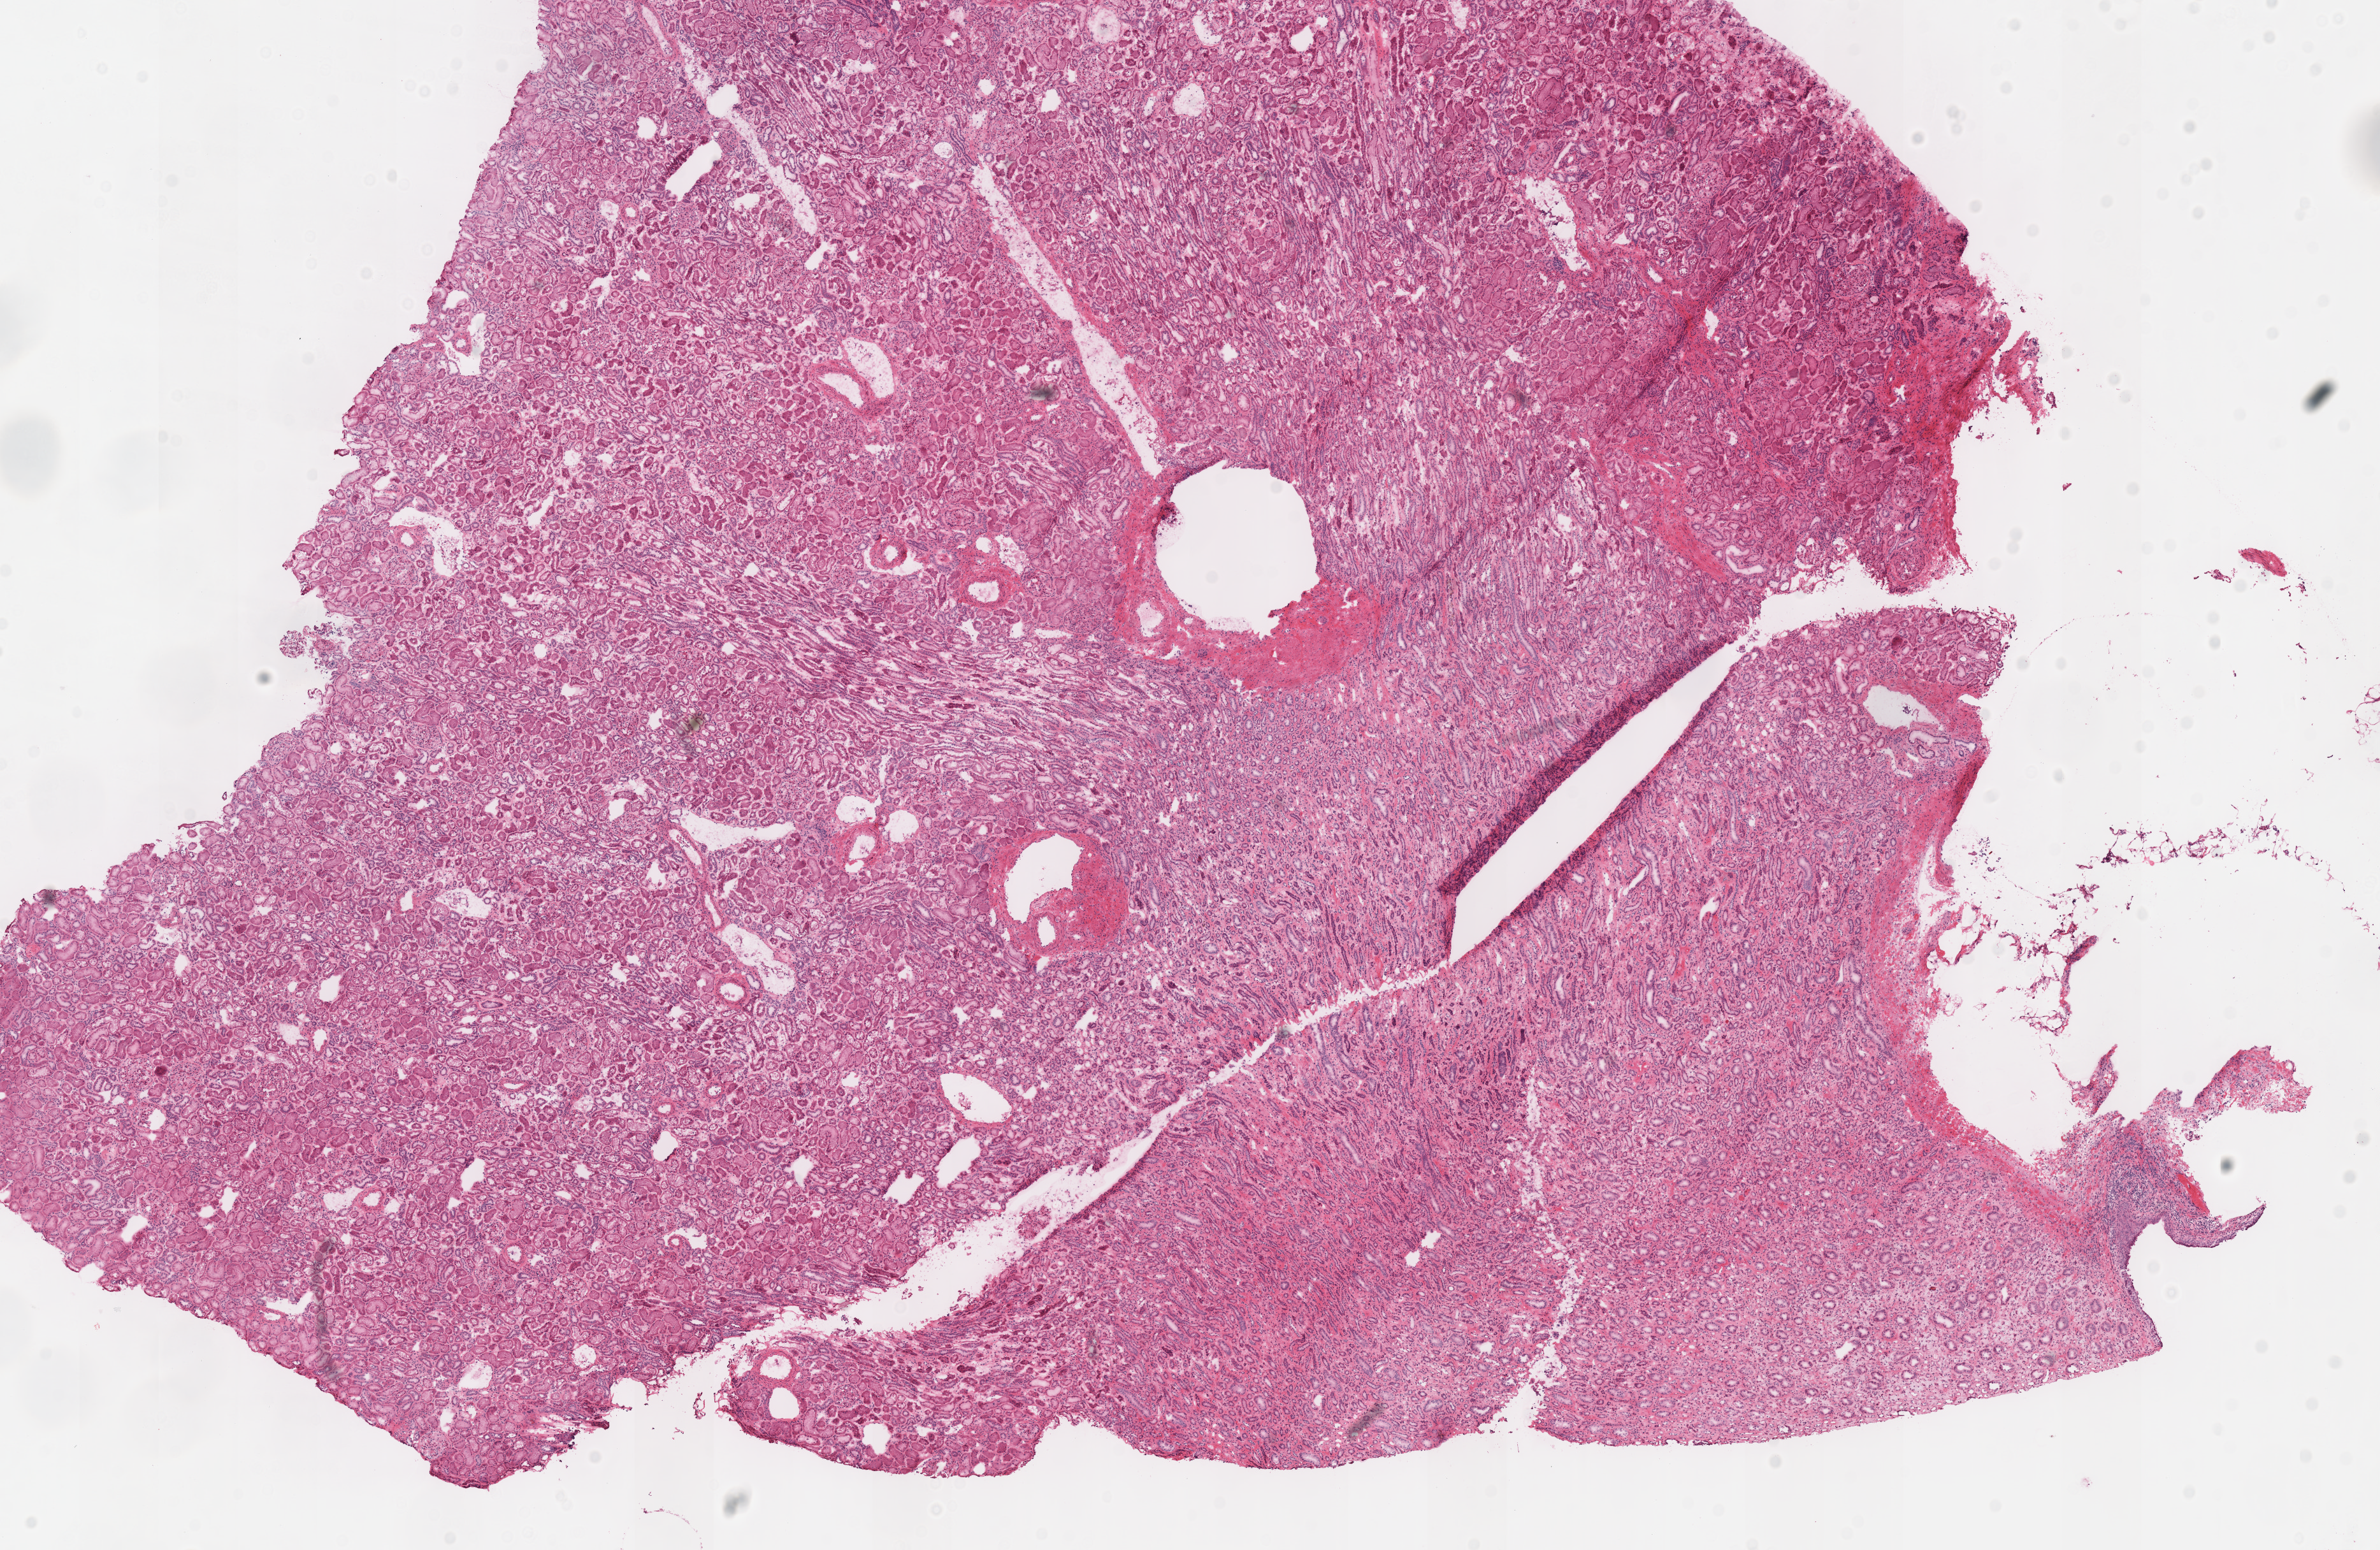
Digitized H&E tissue section (whole slide), whole scanned area (about 14.7 x 9.6 mm) shown as a low-resolution overview. Frozen section from the top of the tissue portion. Solid tissue normal (non-tumour tissue) sample from the kidney. Patient: male, age at initial diagnosis 41 years.
* this section: solid tissue normal (non-tumour) sample from the same patient
* patient diagnosis: Renal cell carcinoma, chromophobe type